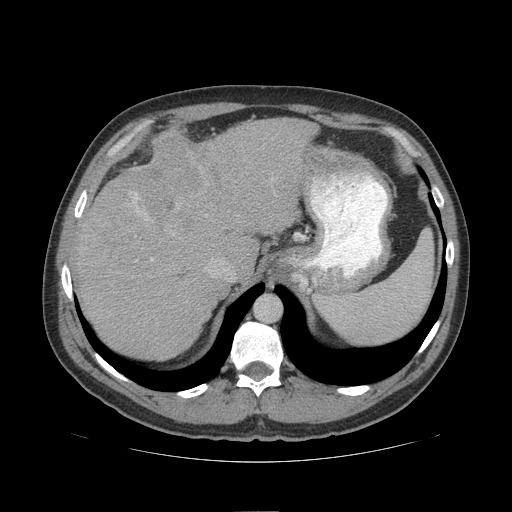
Contrast-enhanced abdominal CT (liver protocol), one axial slice; reconstruction kernel STANDARD; soft-tissue window (W 400 / L 40 HU); 2.5 mm slice thickness; 512 × 512 image matrix. Case-level facts recorded for this patient, not image findings: diagnosis: hepatocellular carcinoma (patient treated with transarterial chemoembolisation; whether this scan precedes or follows treatment is not stated here); TNM stage (as recorded): Stage-IIIB; Child-Pugh class: A; tumour differentiation: poorly differentiated; tumour nodularity: multinodular.
Structures marked on this image (semi-automatically segmented with operator editing):
- abdominal aorta: bounding box [x1, y1, x2, y2] px = [256, 295, 281, 322]
- liver parenchyma outside the tumour (the mass and vessels are separate outlines, so this box may not span the whole liver): [72, 118, 316, 360]
- mass: [112, 130, 211, 233]
- liver vessels: [151, 258, 153, 260]